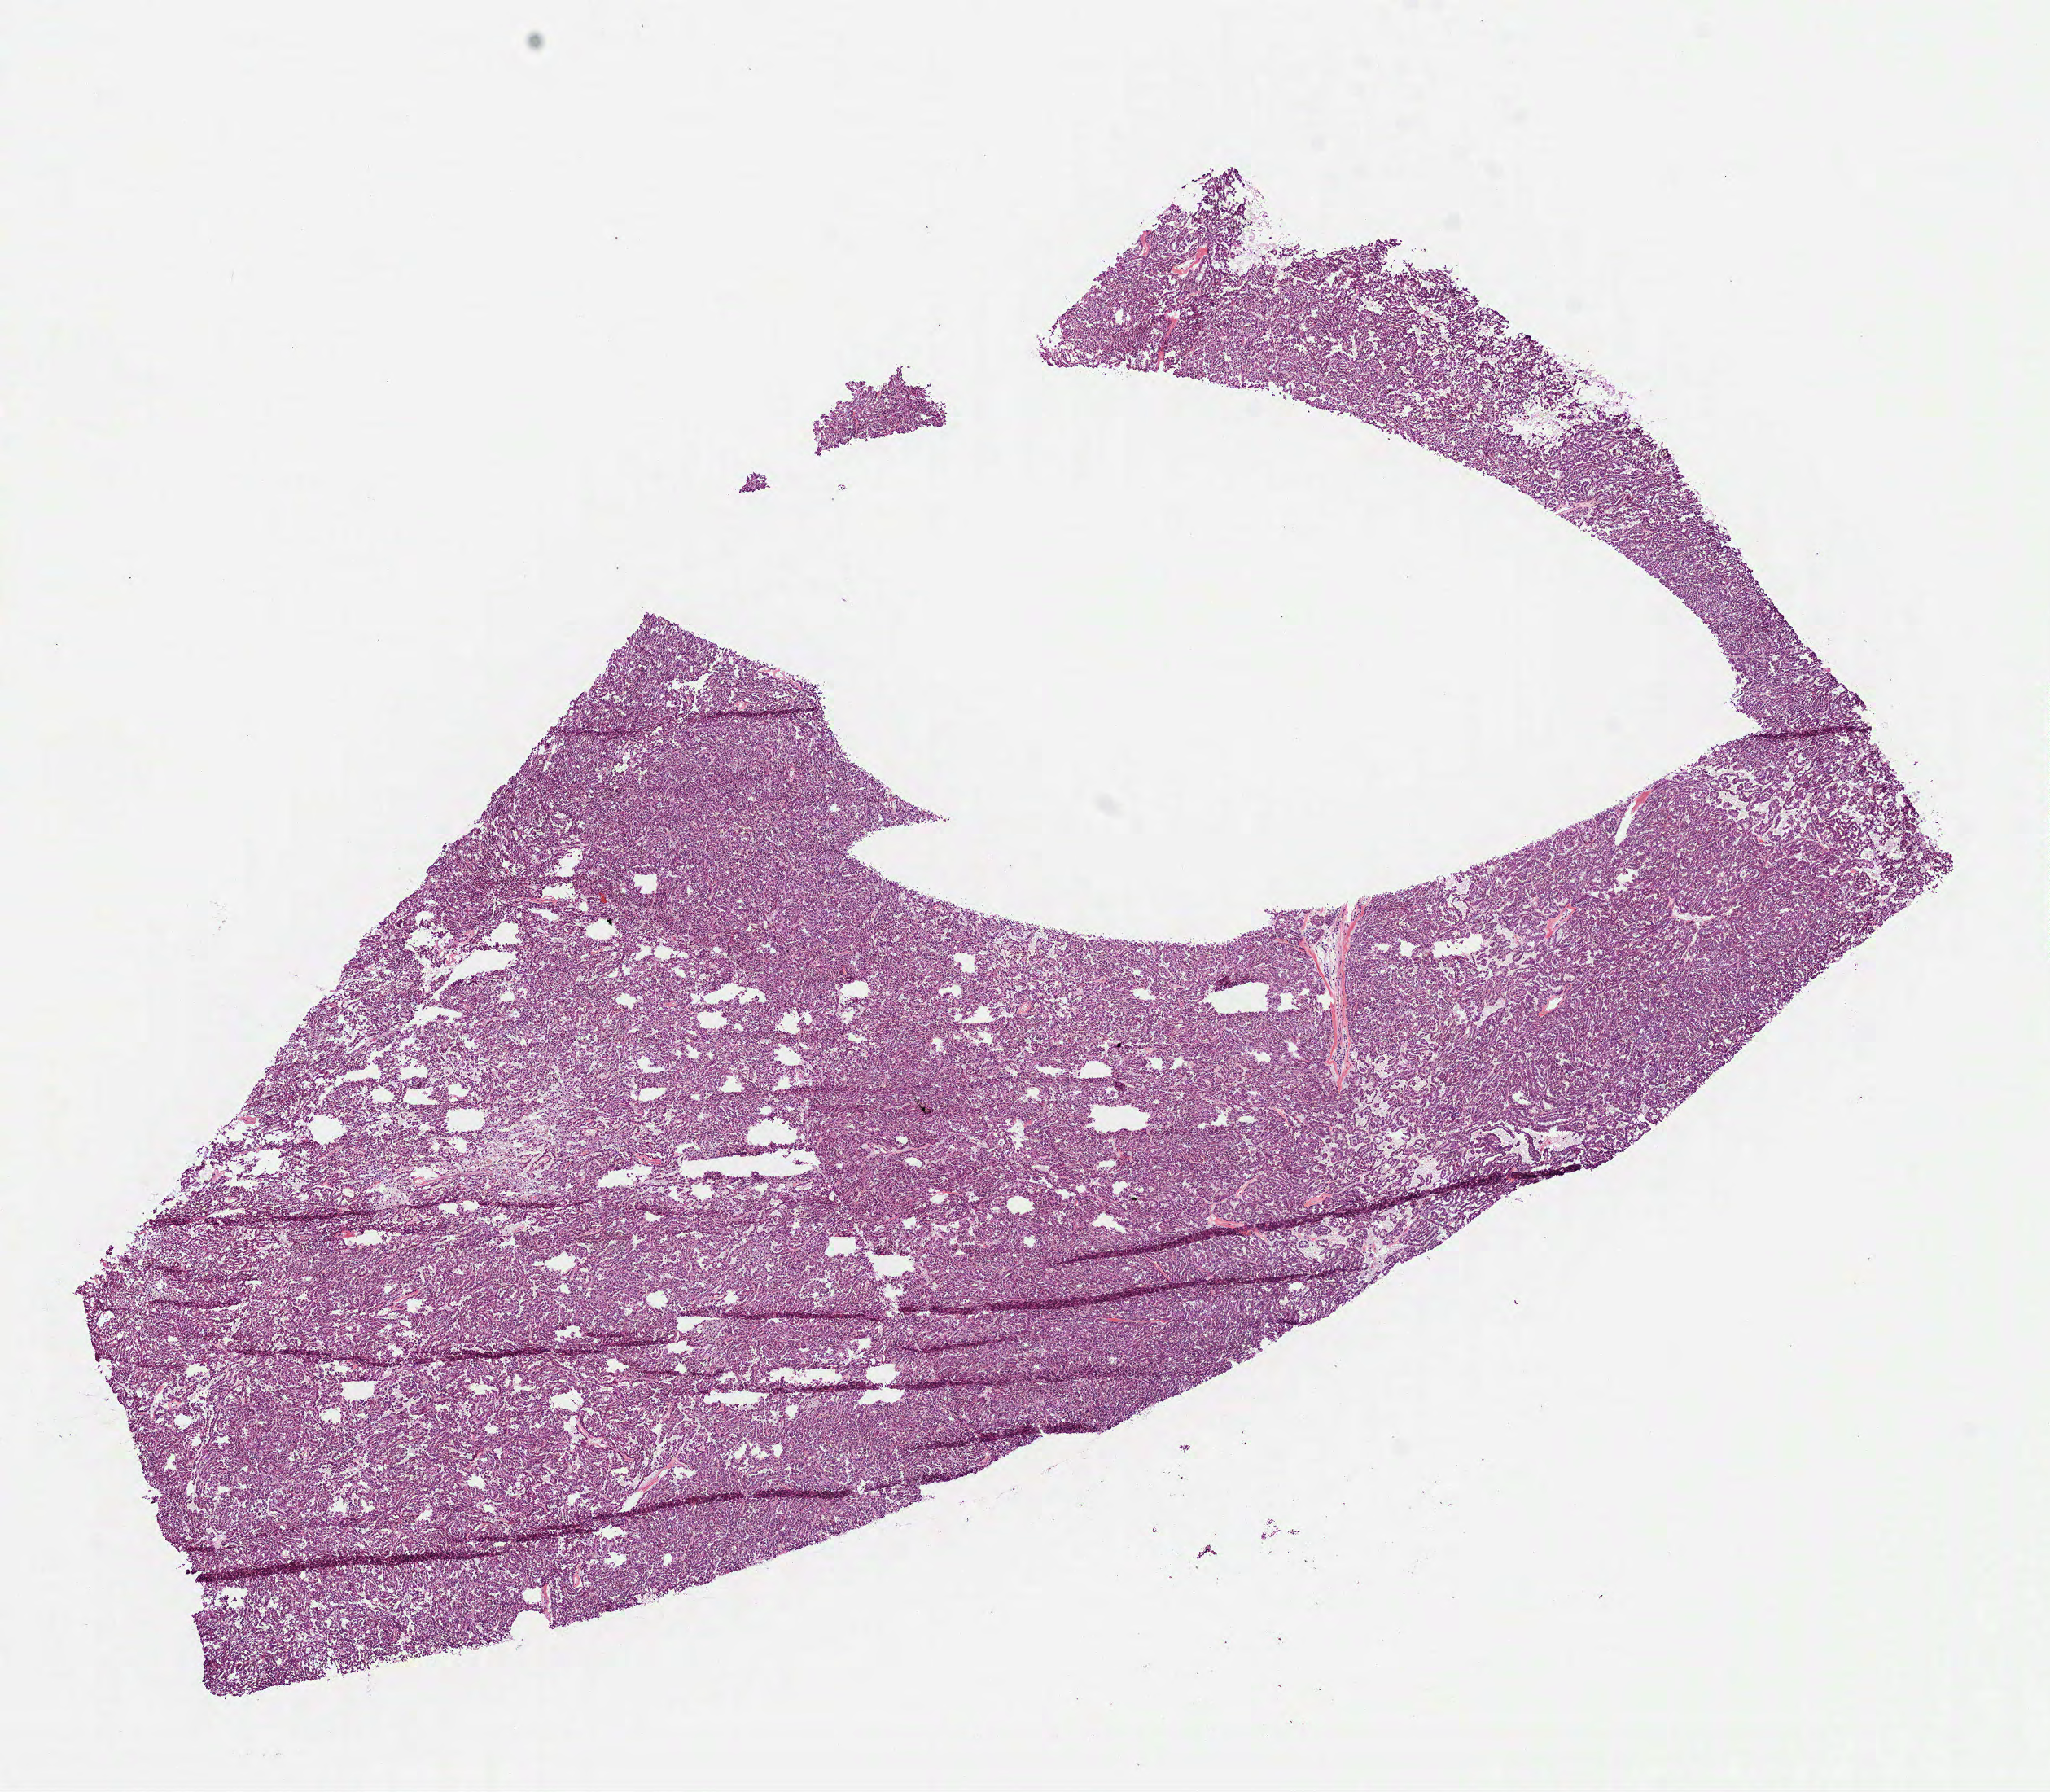
Digitized Hematoxylin and eosin (H&E) stained tissue section (whole slide) — shown as a low-resolution overview of the whole scanned area (about 10.2 x 8.9 mm). Frozen section from the bottom of the tissue portion. Primary tumour sample from the kidney. Patient: male, age at initial diagnosis 59 years. Composition of this section per pathologist review: tumour cells 100%, tumour nuclei 90%, normal cells 0%, stromal cells 0%, necrosis 0%. Infiltration values recorded for this section: lymphocyte infiltration 0%, monocyte infiltration 1%, neutrophil infiltration 0%.
Pathologic diagnosis: Papillary adenocarcinoma, NOS. AJCC pathologic stage: II (7th edition).